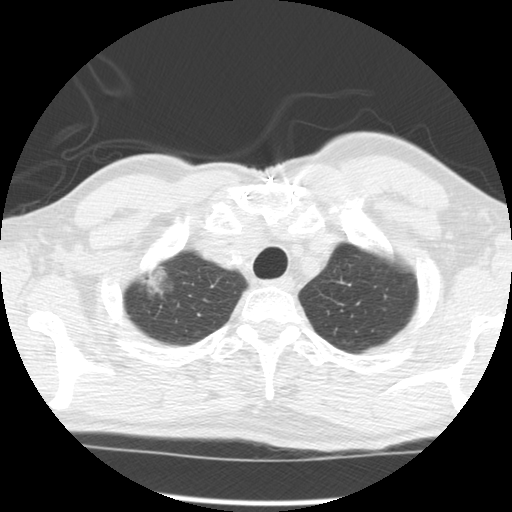
Low-dose screening chest CT, axial slice. Second annual screen. Lung window (W 1500 / L -600 HU). 2.5 mm slice thickness. Standard (soft-tissue) reconstruction kernel (STANDARD). Slice 13 of 120 in the series. 512 × 512 image matrix. Male, age 64 years at enrolment. Former smoker at enrolment.
Expert-annotated lung lesion, box from (x=122, y=244) to (x=180, y=310) px. The screening reader recorded 2 non-calcified nodules or masses ≥4 mm on this exam (right upper lobe, left upper lobe); which of them this box marks is not recorded. Official screen result: positive, other. Later outcome: lung cancer diagnosed 429 days after this screen — adenocarcinoma, NOS, right upper lobe, well differentiated (G1), stage IB (AJCC 6th edition), 45 mm at pathology.